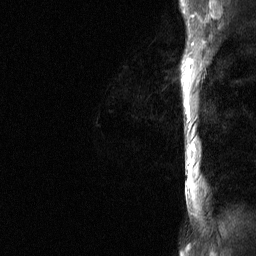
Breast MRI (dynamic contrast-enhanced), one sagittal slice; slice 51 of 64 in the series (ordered by position); dynamic contrast-enhanced study with each time point stored as its own series, time point 2 of 3 at this slice position (early post-contrast, ordered by acquisition time); 1.5 T; TE 4.8 ms, TR 27 ms; 2 mm slice thickness; 256 × 256 image matrix, field of view 200 × 200 mm. Female patient, age 36 years. Case-level facts recorded for this patient, not image findings: setting: breast cancer imaged before/during neoadjuvant chemotherapy; receptor status: HR-positive, HER2-negative.
Outlined on this slice (semi-automatic segmentation, software-assisted and operator-edited):
- analysis volume of interest (the breast-tissue region the enhancement analysis was run in; not a lesion): bounding box [x1, y1, x2, y2] px = [181, 56, 187, 205]
- tumour enhancement mask (voxels above the 90 % enhancement threshold inside the analysis volume of interest): [184, 66, 187, 110]